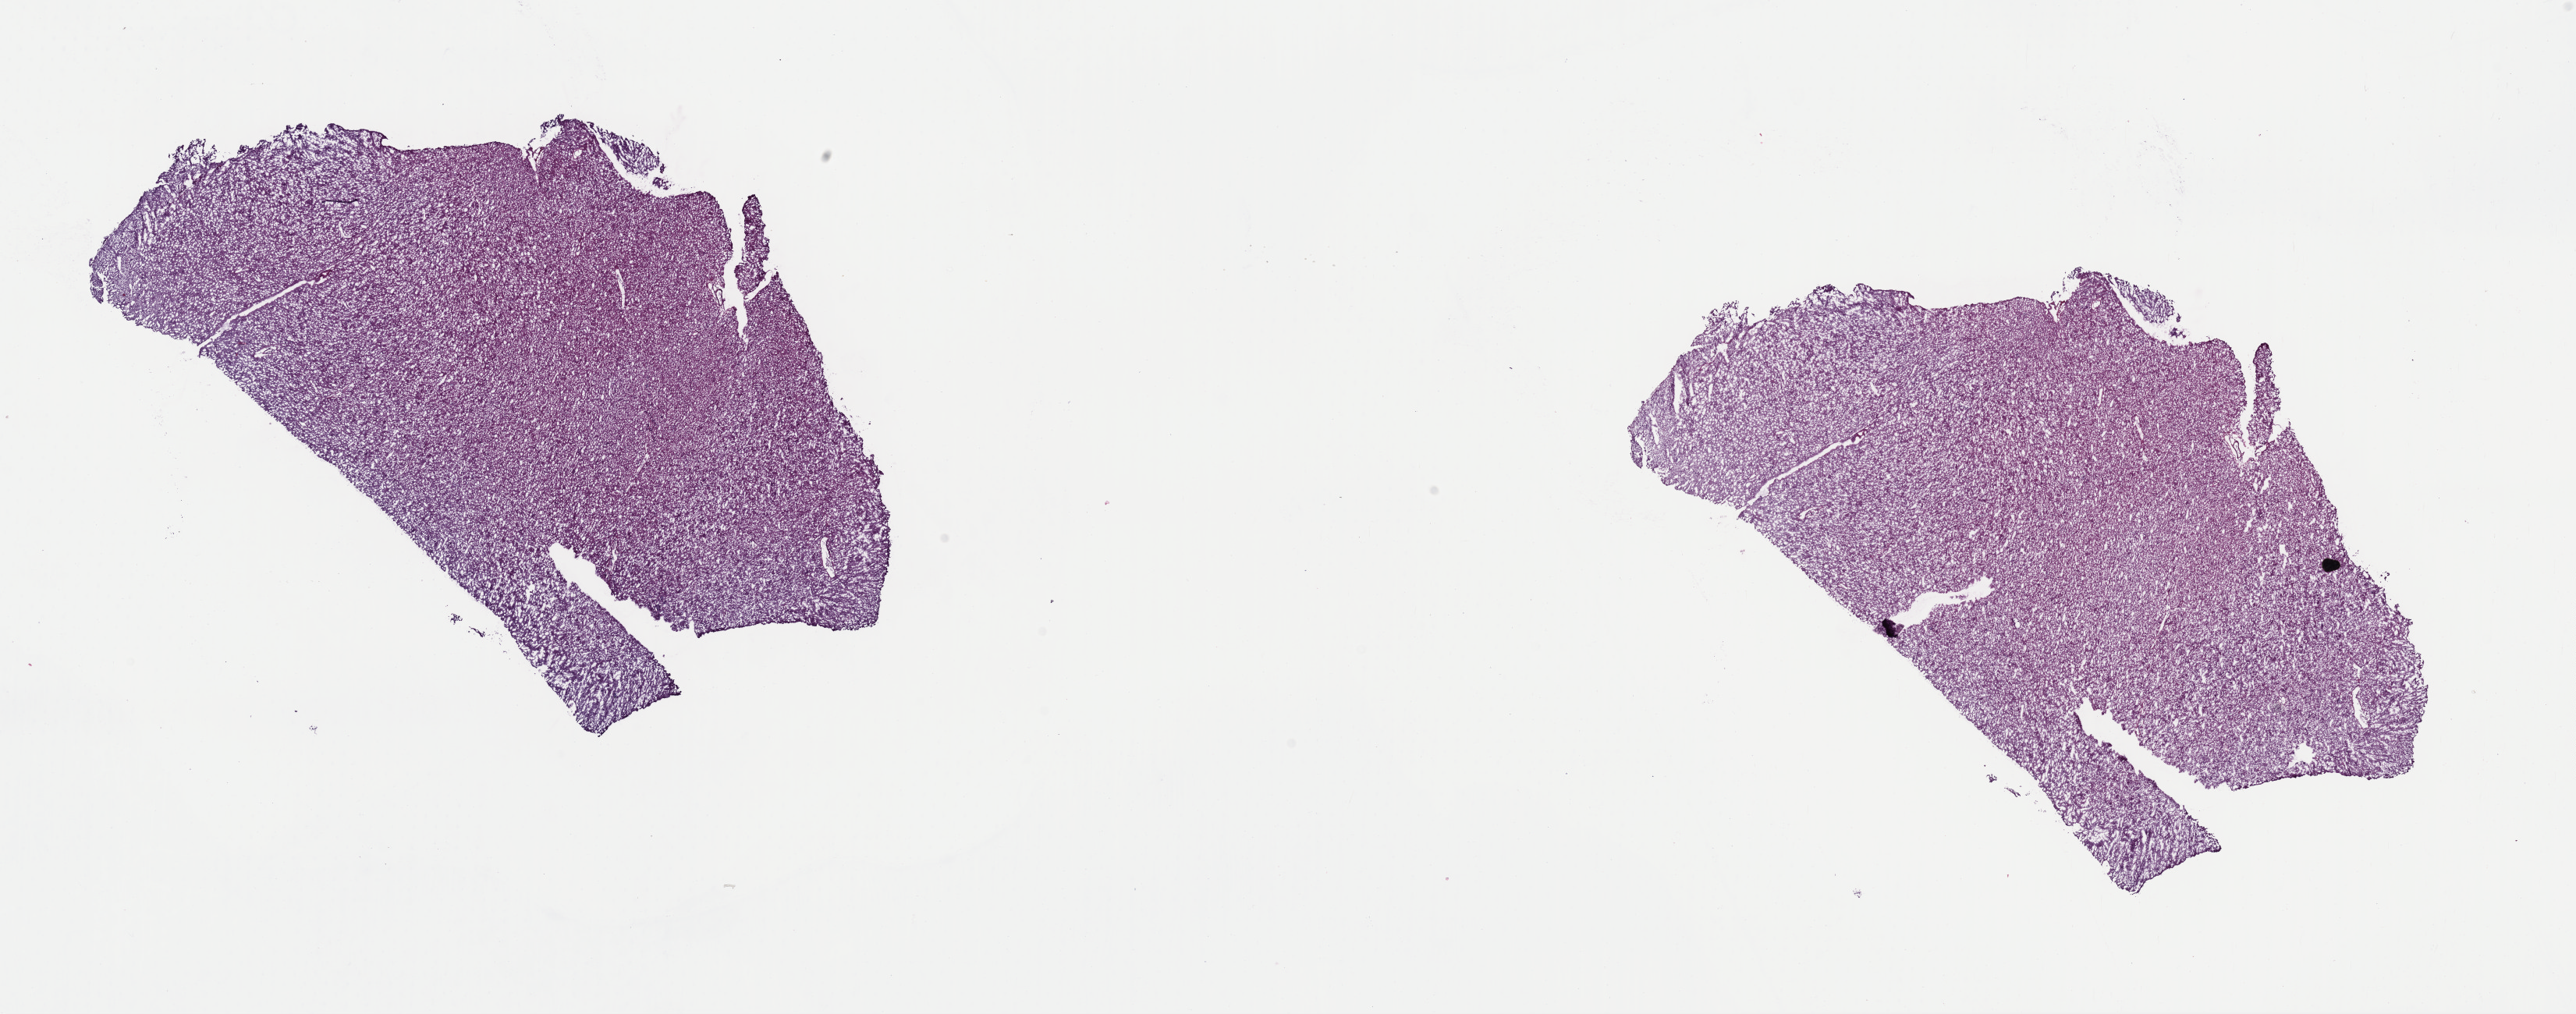
Digitized H&E tissue section (whole slide), low-resolution overview of the scanned area, about 26.1 x 10.3 mm. Frozen section from the top of the tissue portion. Brain, primary tumour sample. Male patient; age at initial diagnosis 21 years. Composition of this section per pathologist review: tumour cells 20%, tumour nuclei 90%.
Histologic diagnosis: Astrocytoma, NOS.